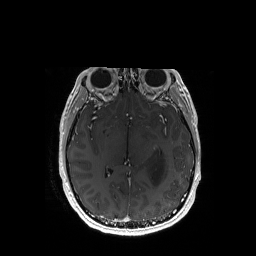
Brain MRI from a brain-tumour surgery series, one axial slice. Slice 94 of 192 in the series (ordered by position). T1-weighted post-contrast. 1 mm slice thickness. 256 × 256 image matrix. Case-level facts recorded for this patient, not image findings: histopathology: Astrocytoma; WHO grade: 3.
Annotated regions visible in this slice (outlined manually by an expert reader):
- tumour: bounding box (x1, y1, x2, y2) in pixels: (148, 148, 165, 185)